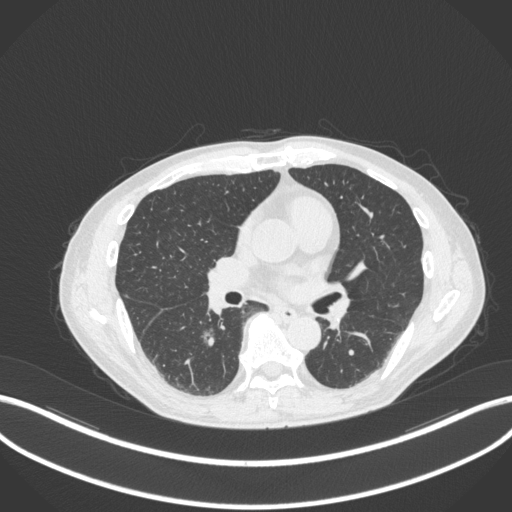
Chest CT, one axial slice. Position 166 of 324 along the scan axis. Lung window (W 1500 / L -600 HU). 1 mm slice thickness. 512 × 512 image matrix, field of view 400 × 400 mm. Male patient, age 61 years. Case-level facts recorded for this patient, not image findings: clinical TNM (as recorded): T1c N0 M0.
Outlined on this slice (rectangle marked by the reading radiologist):
- lung tumour (recorded histology: adenocarcinoma): bounding box <201,323,219,350> (left, top, right, bottom; pixels)